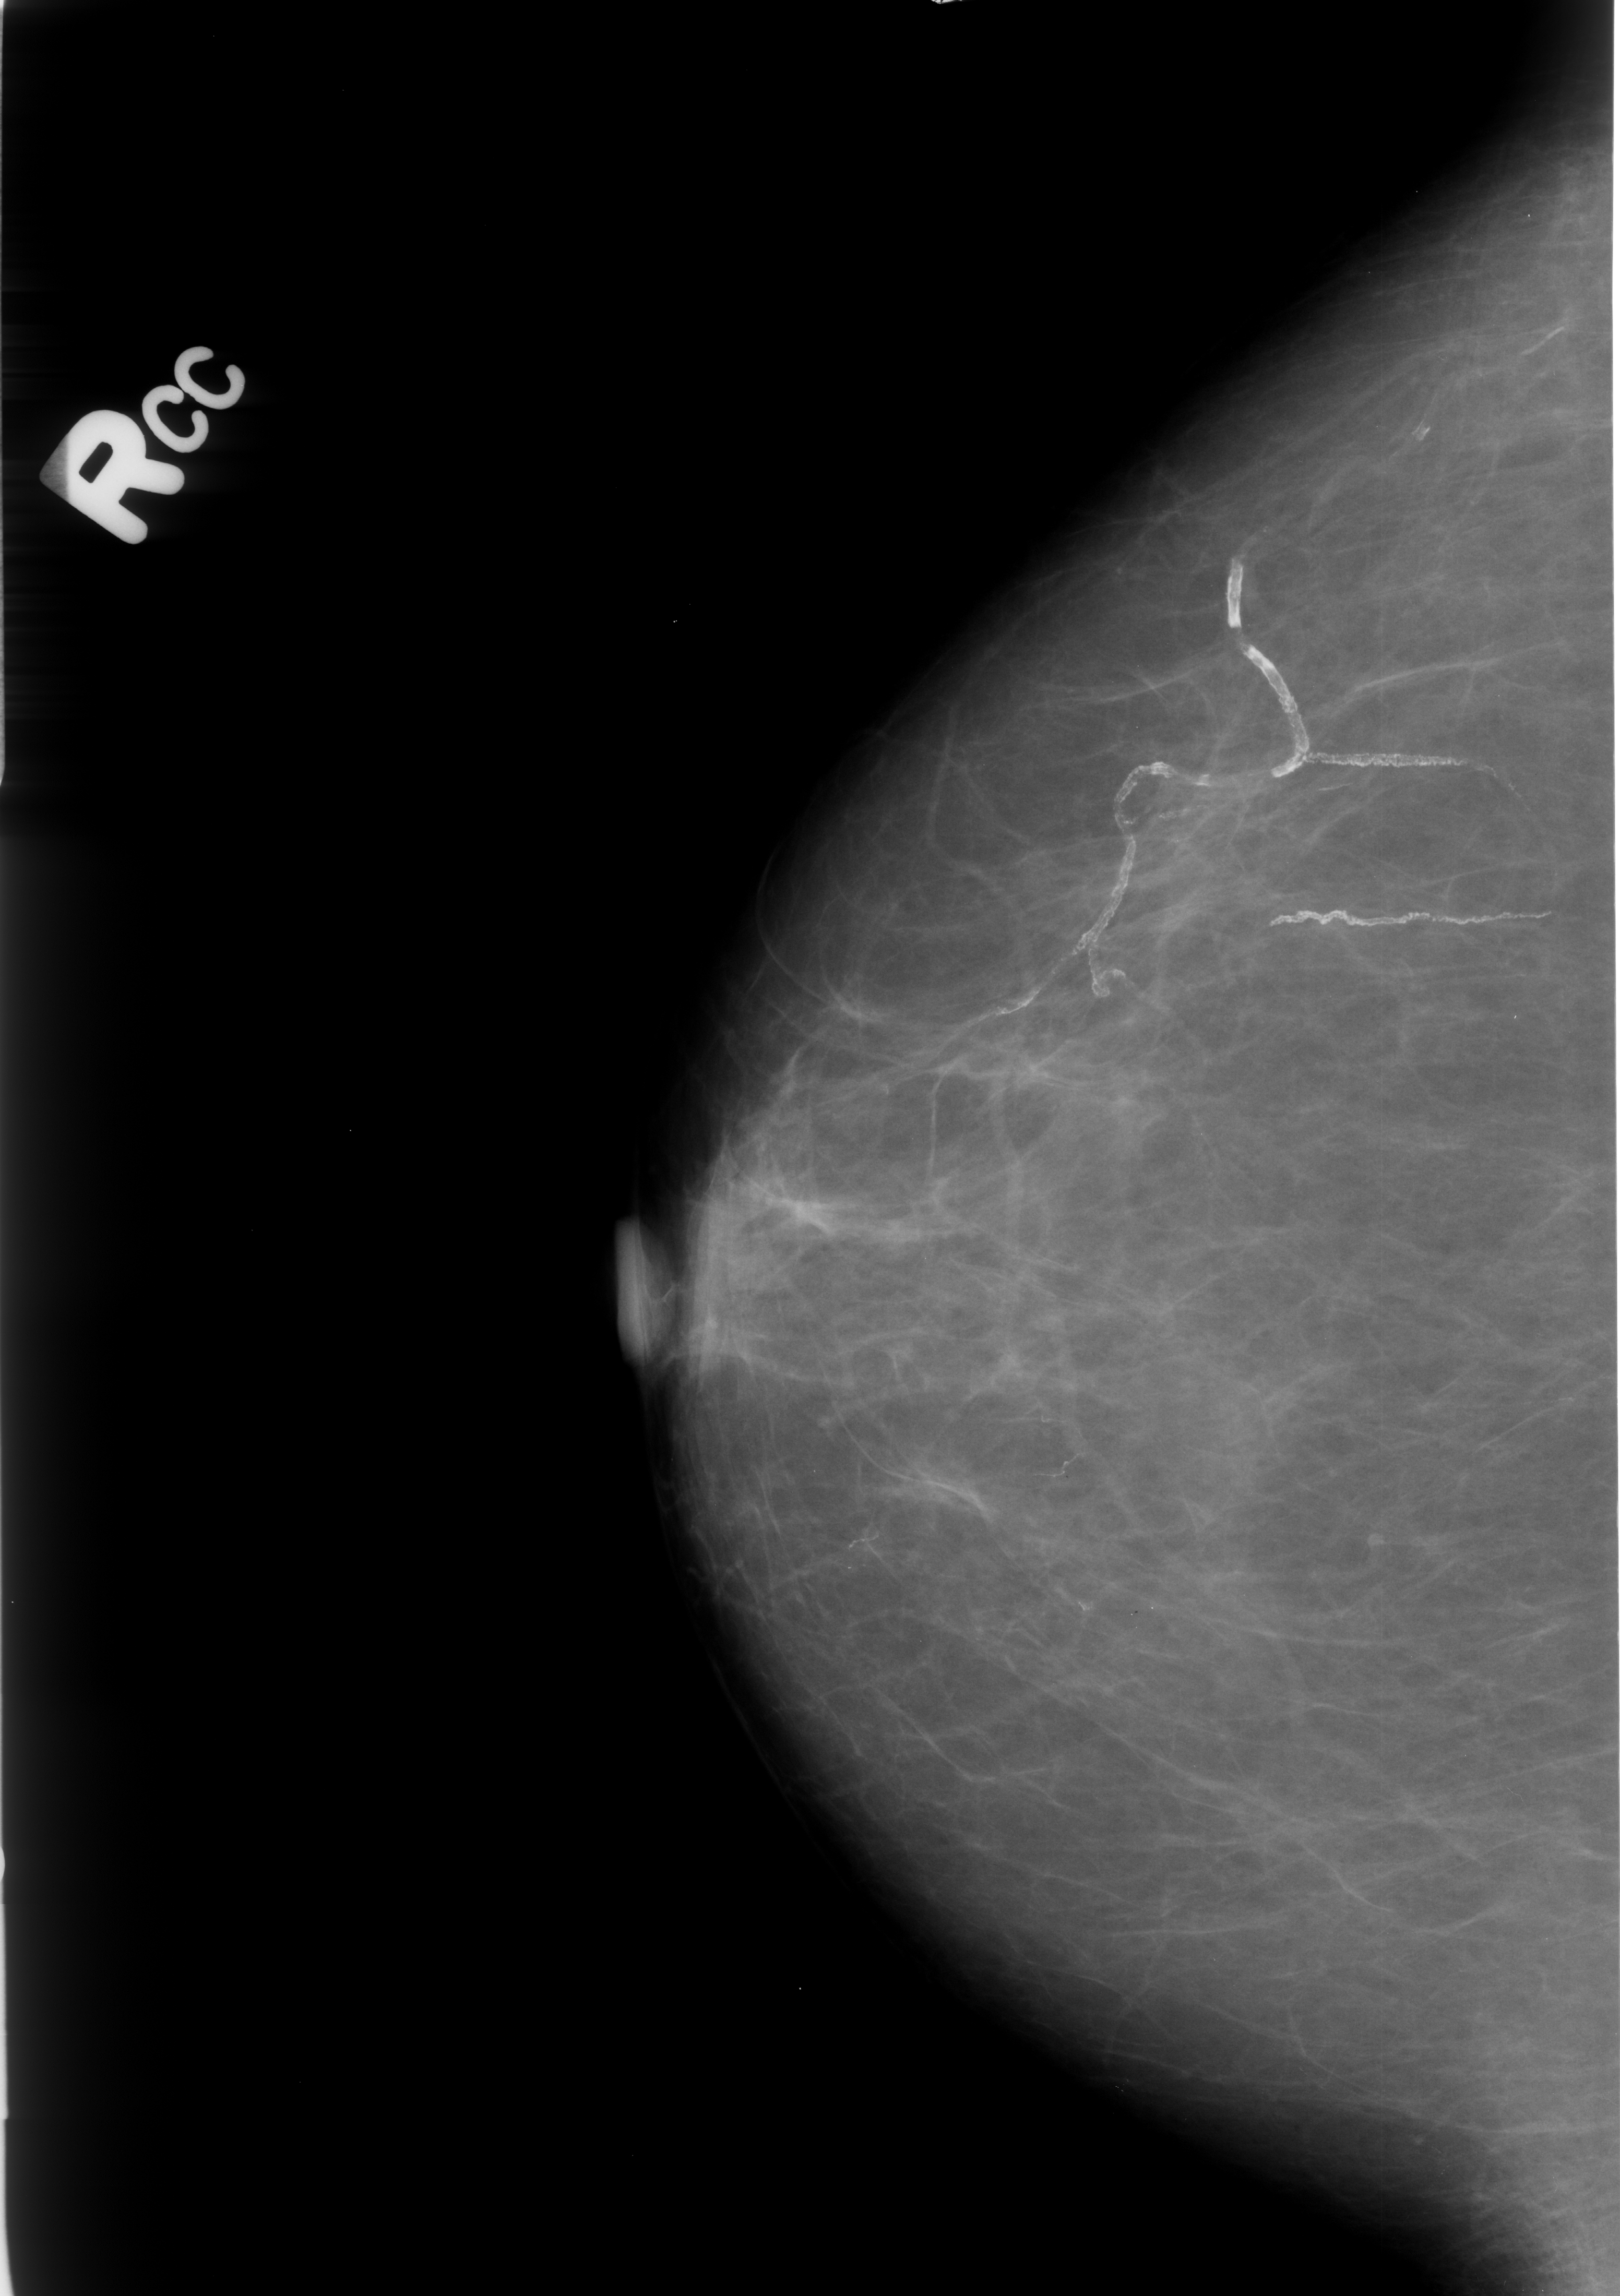
Mammogram (digitized film). Right breast. Craniocaudal (CC) view. BI-RADS breast density category 1 (scale 1–4). 1620 × 2296 image matrix.
Marked abnormalities (boxes around the expert regions of interest):
- Finding 1 of 5: calcifications, morphology fine linear branching; BI-RADS assessment category 2; outcome (as recorded, no biopsy): benign without callback (not worked up further): bounding box <810,1511,907,1583> (left, top, right, bottom; pixels)
- Finding 2 of 5: calcifications, morphology vascular; BI-RADS assessment category 2; subtlety rating 4 on a 1 (subtle) to 5 (obvious) scale; outcome (as recorded, no biopsy): benign without callback (not worked up further): <868,429,1316,1149>
- Finding 3 of 5: calcifications, morphology fine linear branching; BI-RADS assessment category 2; benign; no additional work-up was recommended (outcome (as recorded, no biopsy): benign without callback): <1031,1369,1091,1416>
- Finding 4 of 5: calcifications, morphology fine linear branching; BI-RADS assessment category 2; subtlety rating 4 on a 1 (subtle) to 5 (obvious) scale; benign; no additional work-up was recommended (outcome (as recorded, no biopsy): benign without callback): <1043,1427,1103,1496>
- Finding 5 of 5: calcifications, morphology vascular; BI-RADS assessment category 2; benign; no additional work-up was recommended (outcome (as recorded, no biopsy): benign without callback): <1244,726,1583,957>